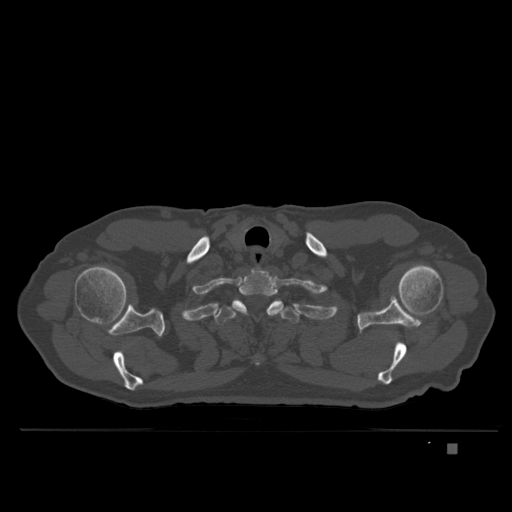
CT including the spine, one axial slice; bone window (W 1800 / L 400 HU); 1.5 mm slice thickness; 512 × 512 image matrix, field of view 434 × 434 mm. Patient: male, 73 years. From the clinical record (not read from this slice): primary cancer: skin.
Structures marked on this image (semi-automatically segmented with operator editing):
- T1 vertebra: bounding box [x1, y1, x2, y2] px = [230, 268, 284, 316]
- T2 vertebra: [215, 299, 299, 365]